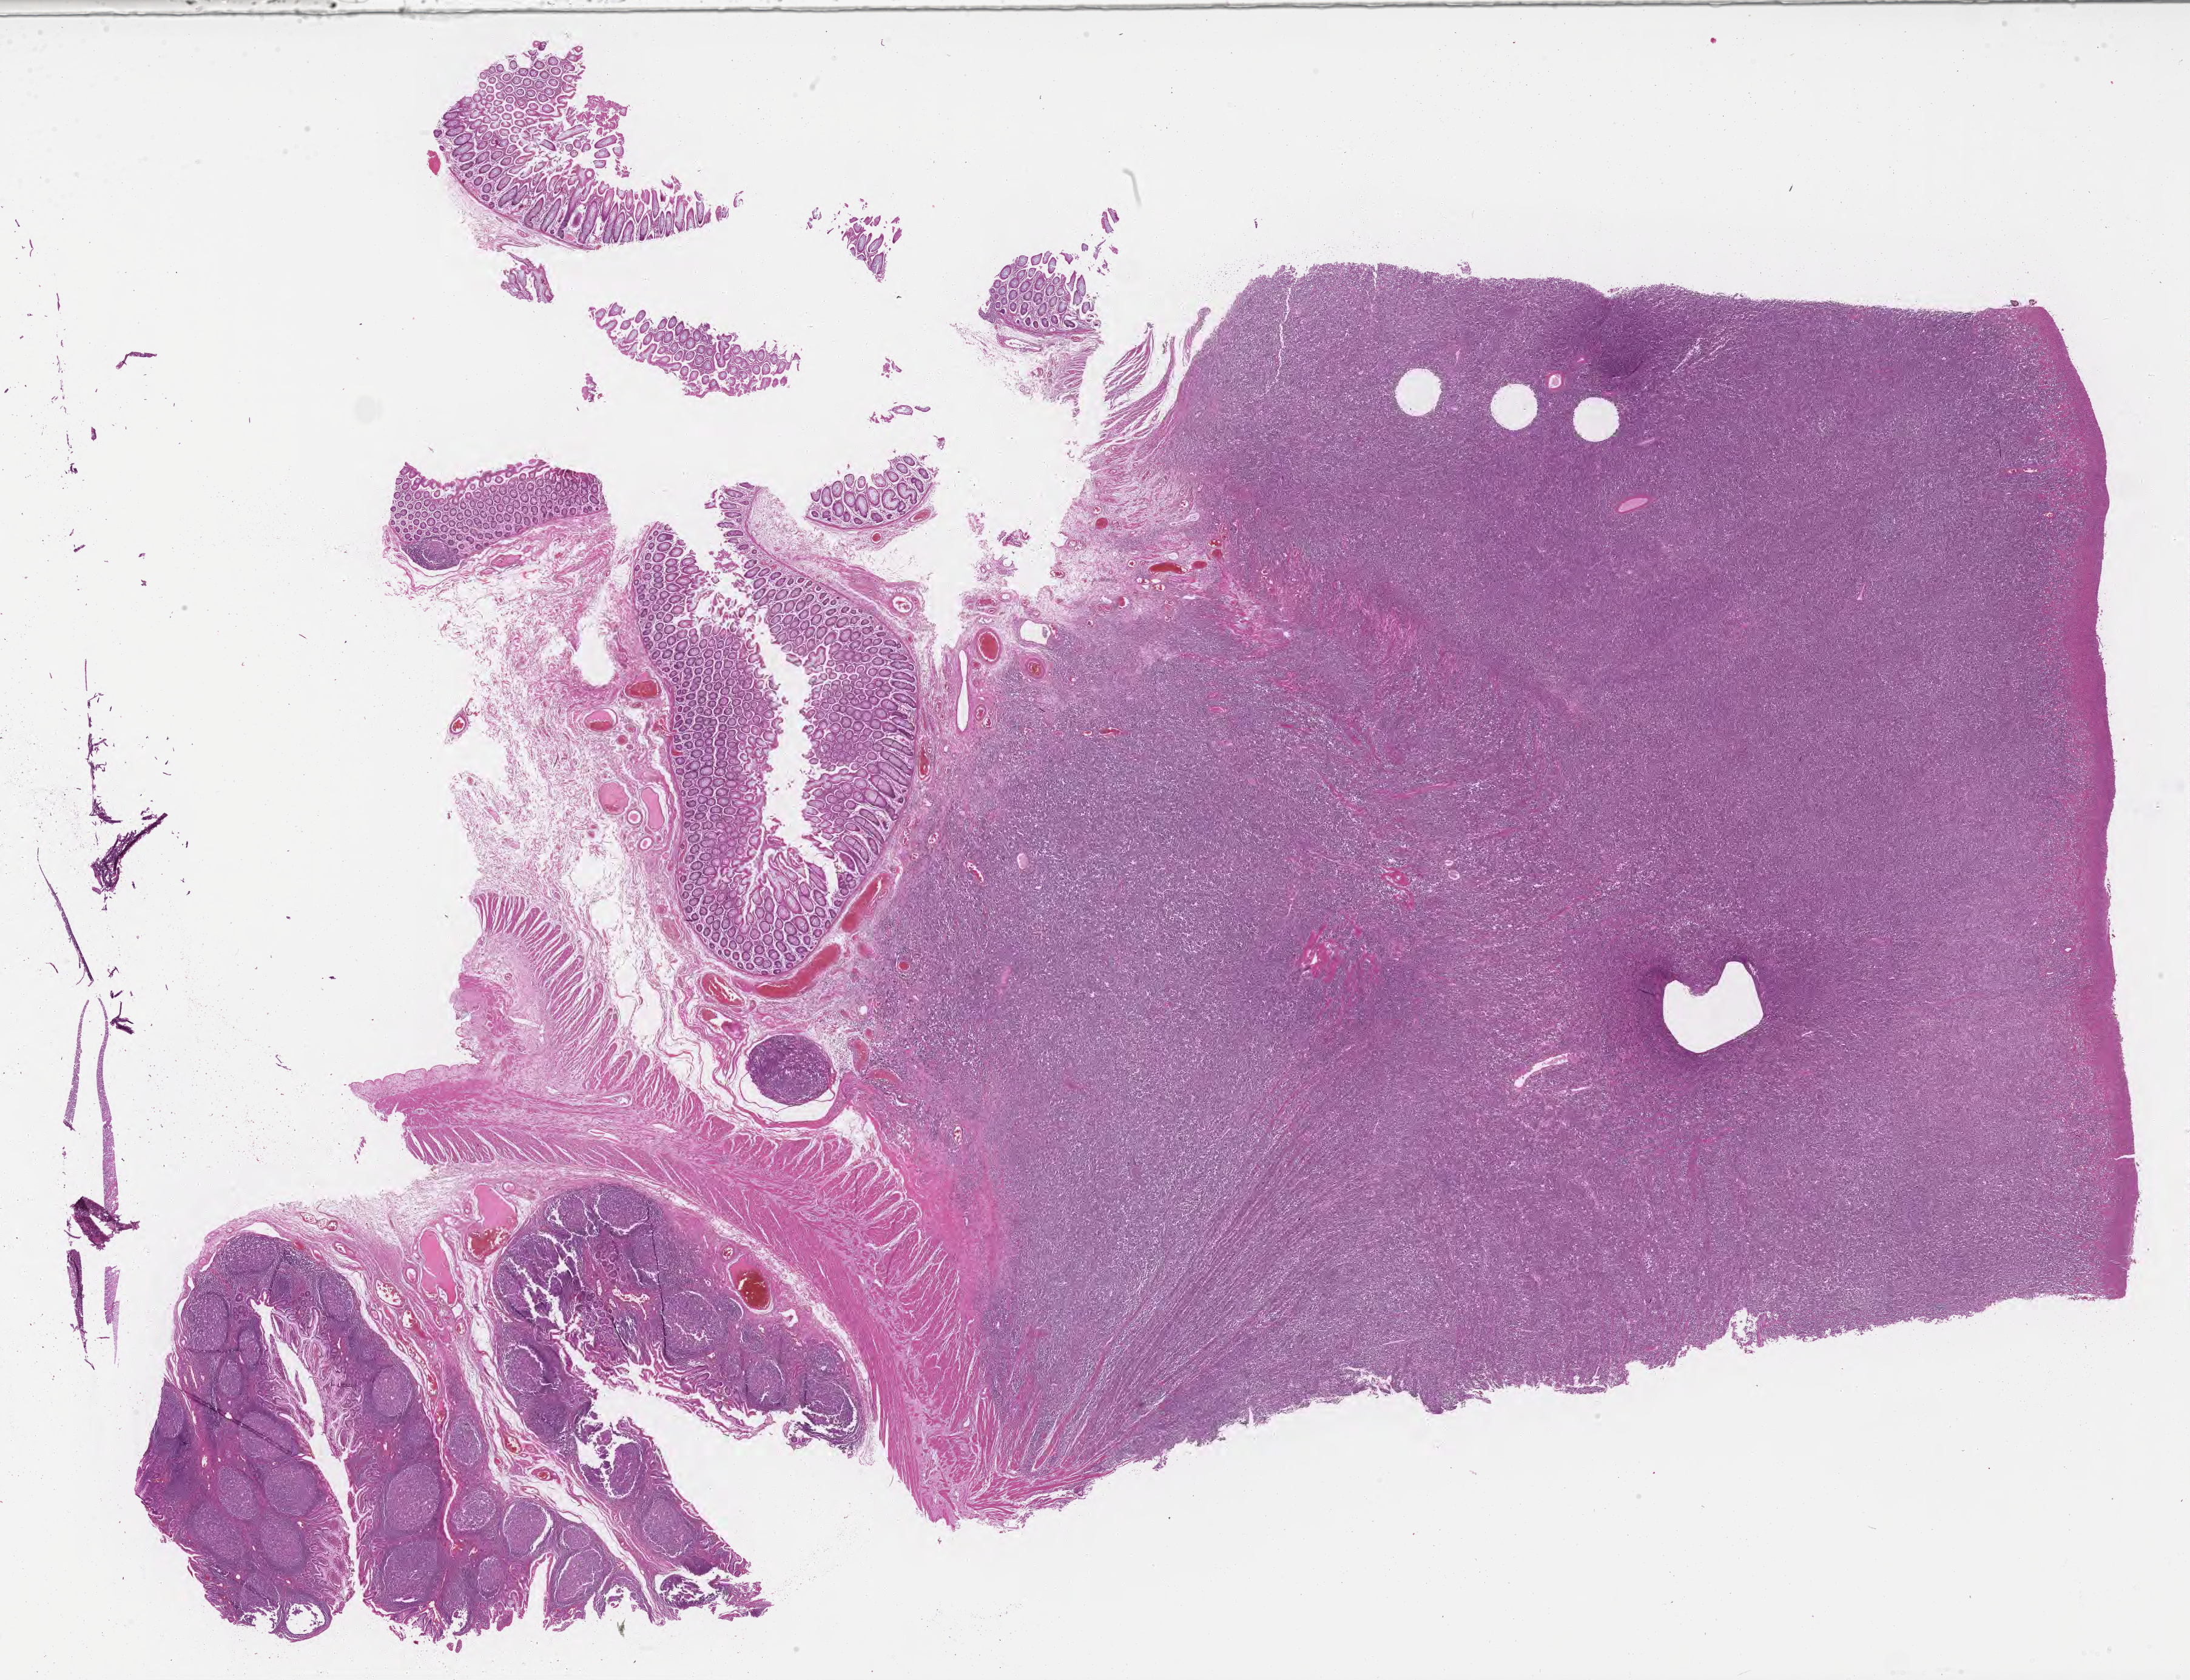
Hematoxylin and eosin (H&E) whole-slide image — whole scanned area (about 29.2 x 22.4 mm) shown as a low-resolution overview, FFPE section, primary tumor. Patient: male, age at initial diagnosis 7 years. Composition of this section per pathologist review: tumor cells 50%, tumor nuclei 75%, stromal cells 5%, necrosis 0%, normal cells 45%. Infiltration values recorded for this section: lymphocyte infiltration 90%, monocyte infiltration 5%, neutrophil infiltration 0%.
Histologic diagnosis: Burkitt lymphoma, NOS. Ann Arbor stage (patient): Stage II.